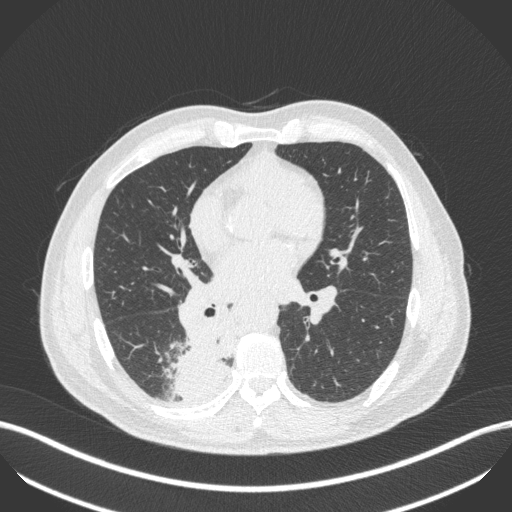
Chest CT, one axial slice; slice 230 of 451 in the series (ordered by position); reconstruction kernel B31f; lung window (W 1500 / L -600 HU); 1 mm slice thickness; 512 × 512 image matrix. Patient: male, 61 years. Case-level facts recorded for this patient, not image findings: clinical TNM (as recorded): T1 N0 M0; histopathological grade: G3.
Annotated regions visible in this slice (bounding box drawn by a radiologist):
- lung tumour (recorded histology: small cell carcinoma): bounding box (x1, y1, x2, y2) in pixels: (161, 320, 230, 403)